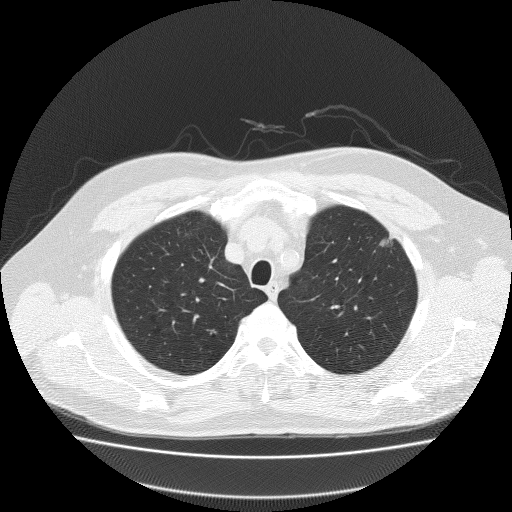
Low-dose screening chest CT, one axial slice. Position 164 of 204 along the scan axis. Reconstruction kernel FC51. 120 kVp. Lung window (W 1500 / L -600 HU). 512 × 512 image matrix, field of view 410 × 410 mm.
Annotated regions visible in this slice (expert manual segmentation):
- lesion 1 (tumor, upper lobe of left lung): bounding box <378,237,390,248> (left, top, right, bottom; pixels)